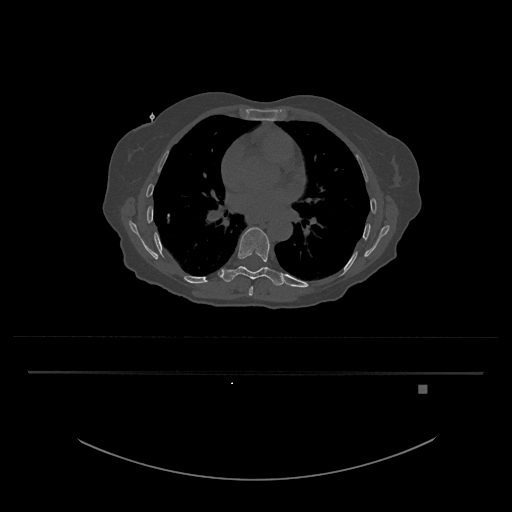
CT including the spine, one axial slice. Position 763 of 797 along the scan axis. Reconstruction kernel Br40s/3. Bone window (W 1800 / L 400 HU). 512 × 512 image matrix. Patient: female, 57 years. Case-level facts recorded for this patient, not image findings: primary cancer: cervical.
Annotated regions visible in this slice (semi-automatic segmentation, software-assisted and operator-edited):
- T8 vertebra: bounding box (x1, y1, x2, y2) in pixels: (248, 286, 253, 296)
- T9 vertebra: (221, 227, 285, 286)